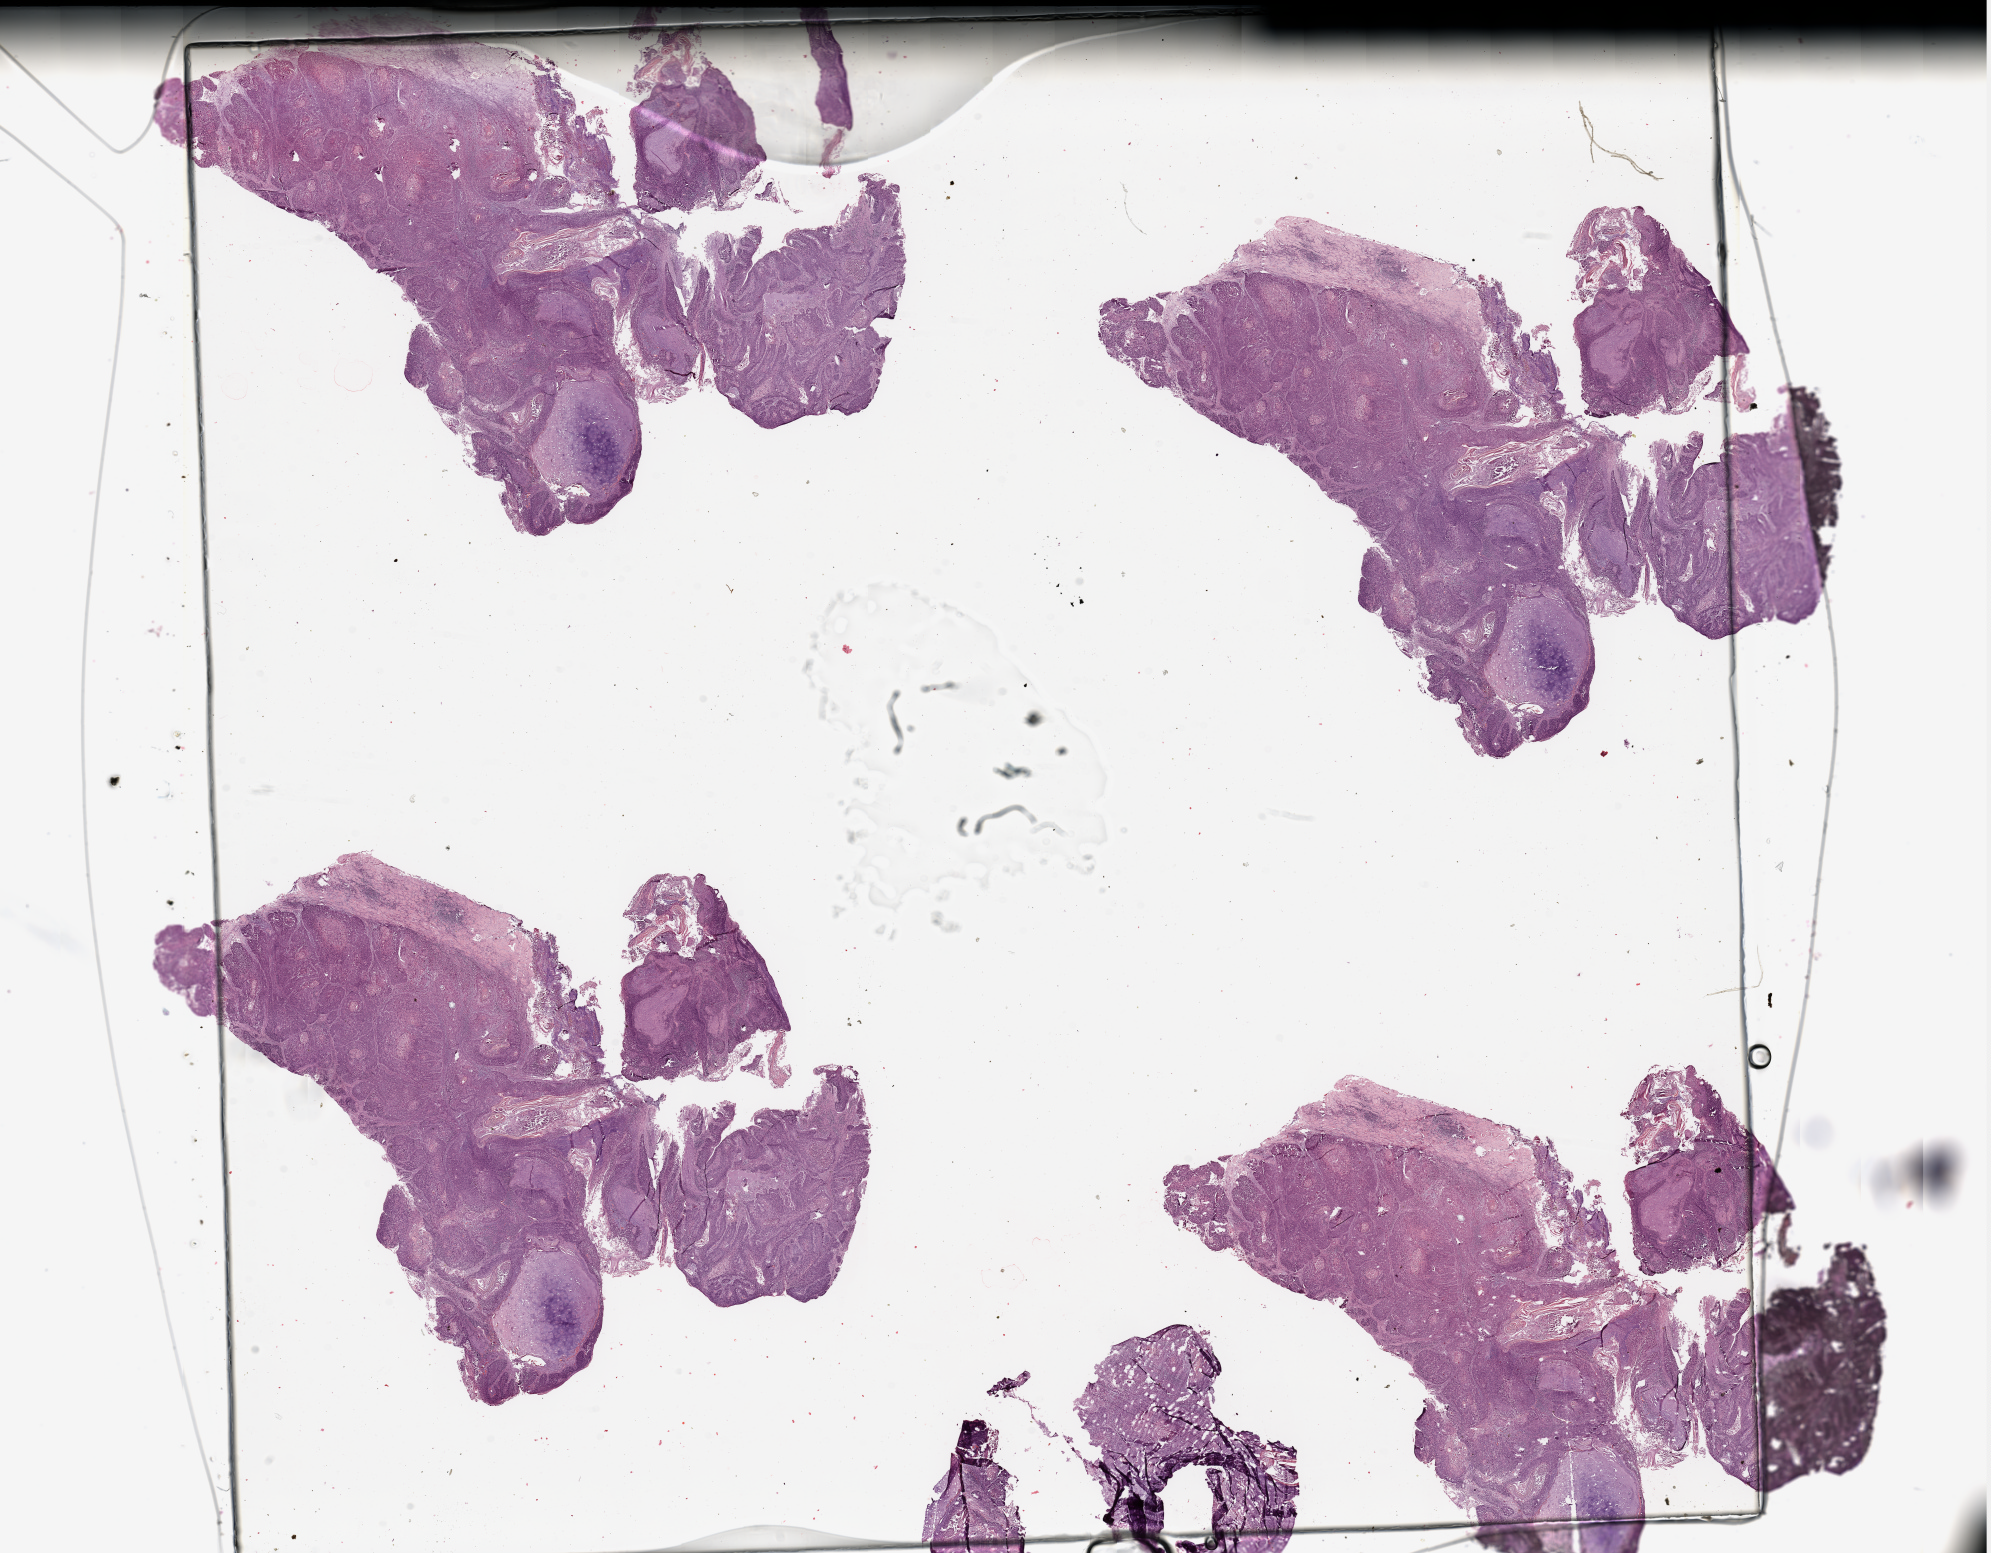
Digitized H&E tissue section (whole slide) — whole scanned area (about 31.5 x 24.6 mm, acquisition: 20x scan) shown as a low-resolution overview. Tumour tissue sample, sampled site: lung. 46-year-old male patient. Histologic grade: G2 (moderately differentiated). Pathologist review of this section (percent, as recorded): tumour nuclei 75%, necrosis 5%.
- AJCC pathologic stage: IIA
- primary tumour site (as recorded): left upper lobe
- diagnosis: Squamous cell carcinoma, NOS